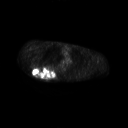
FDG PET of an extremity soft-tissue mass (from a PET/CT study), one axial slice; position 189 of 267 along the scan axis; 3.27 mm slice thickness; 128 × 128 image matrix. Patient: male, 61 years. Case-level facts recorded for this patient, not image findings: histological type: pleiomorphic spindle cell undifferentiated; grade: high; site of the primary tumour: right parascapusular.
Outlined on this slice (expert contour drawn on MRI and transferred to this co-registered scan by the dataset authors):
- gross tumour volume including surrounding oedema: box from (x=32, y=65) to (x=58, y=79) px
- gross tumour volume (mass): (x=32, y=65)–(x=55, y=78)